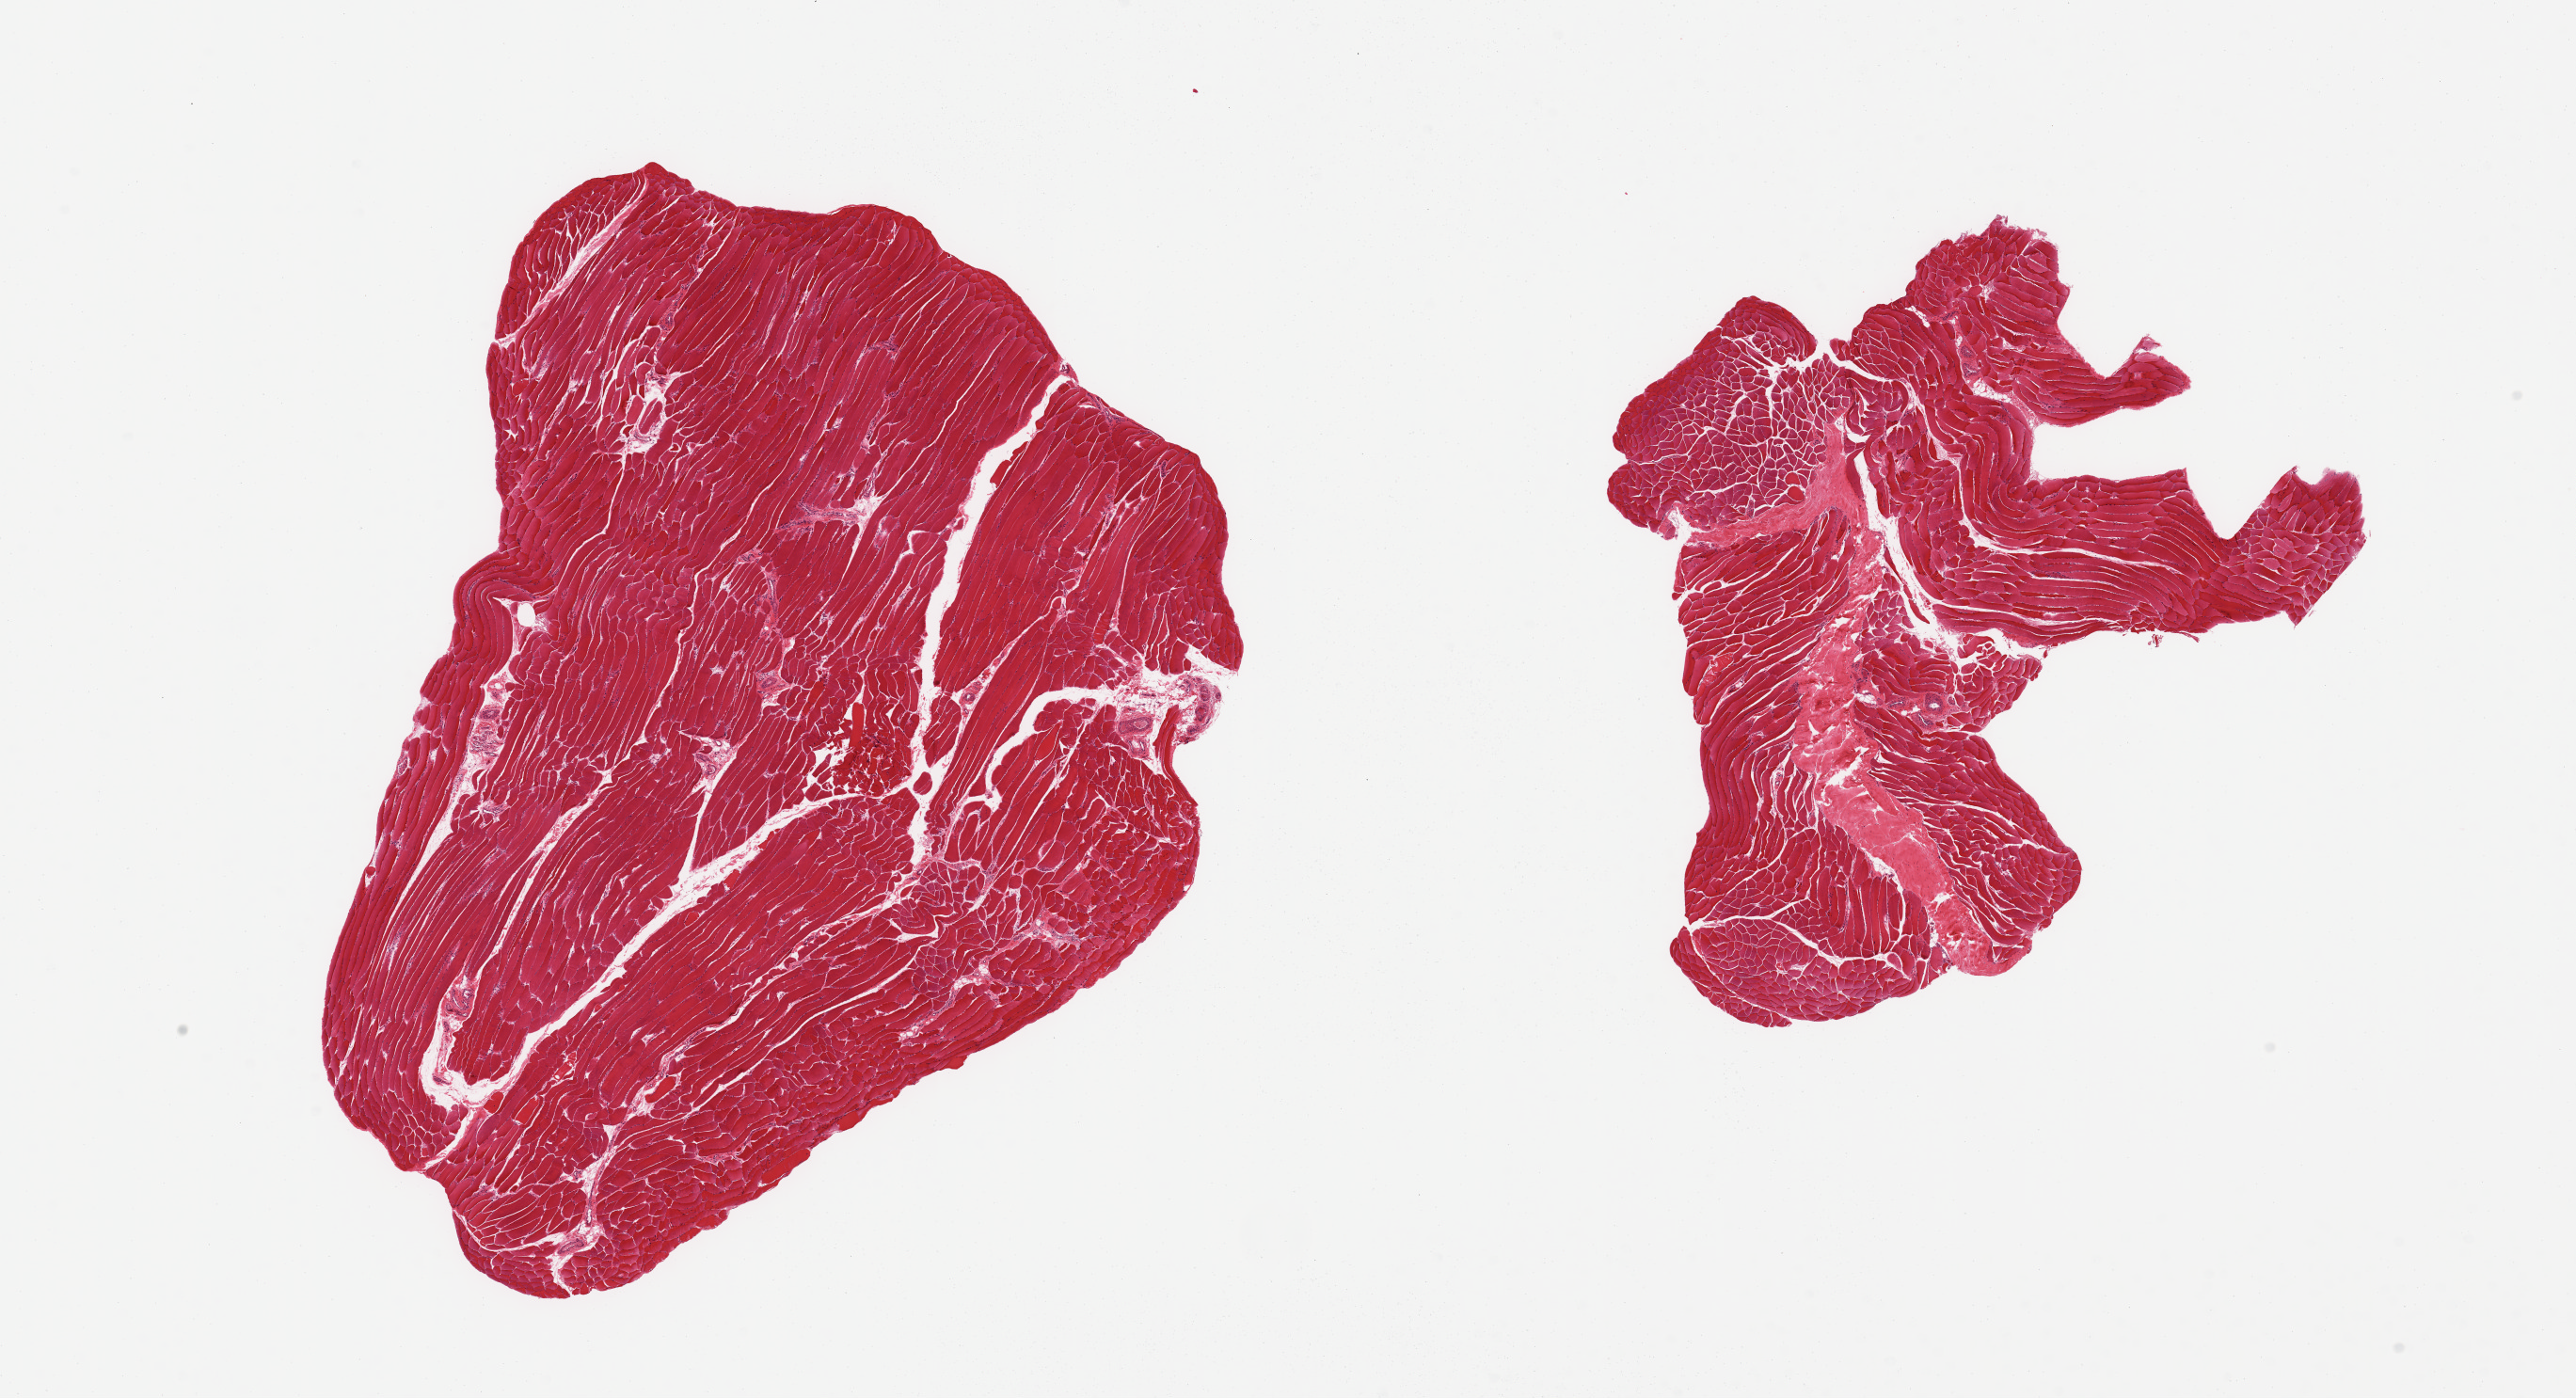
Digitized hematoxylin and eosin (H&E)-stained section, brightfield — whole scanned area (about 21.7 x 11.8 mm) shown as a low-resolution overview; PAXgene-fixed, paraffin-embedded tissue; target tissue: skeletal muscle; tissue donor sample. Donor: male.
Review note (as recorded): 2 pieces, minimal interstitial fat; ~10% tendinous insertion.